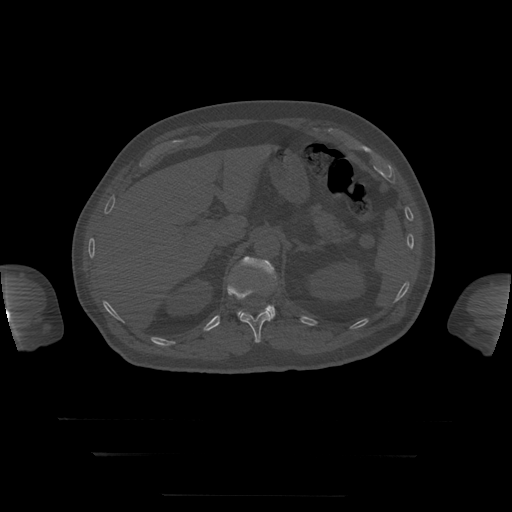
CT including the spine, one axial slice. Slice 65 of 397 in the series (ordered by position). 120 kVp. Bone window (W 1800 / L 400 HU). 512 × 512 image matrix. Patient age 73 years. From the clinical record (not read from this slice): primary cancer: prostate.
Outlined on this slice (semi-automatic segmentation, software-assisted and operator-edited):
- L1 vertebra: box from (x=238, y=257) to (x=276, y=320) px
- T12 vertebra: (x=227, y=284)–(x=271, y=343)